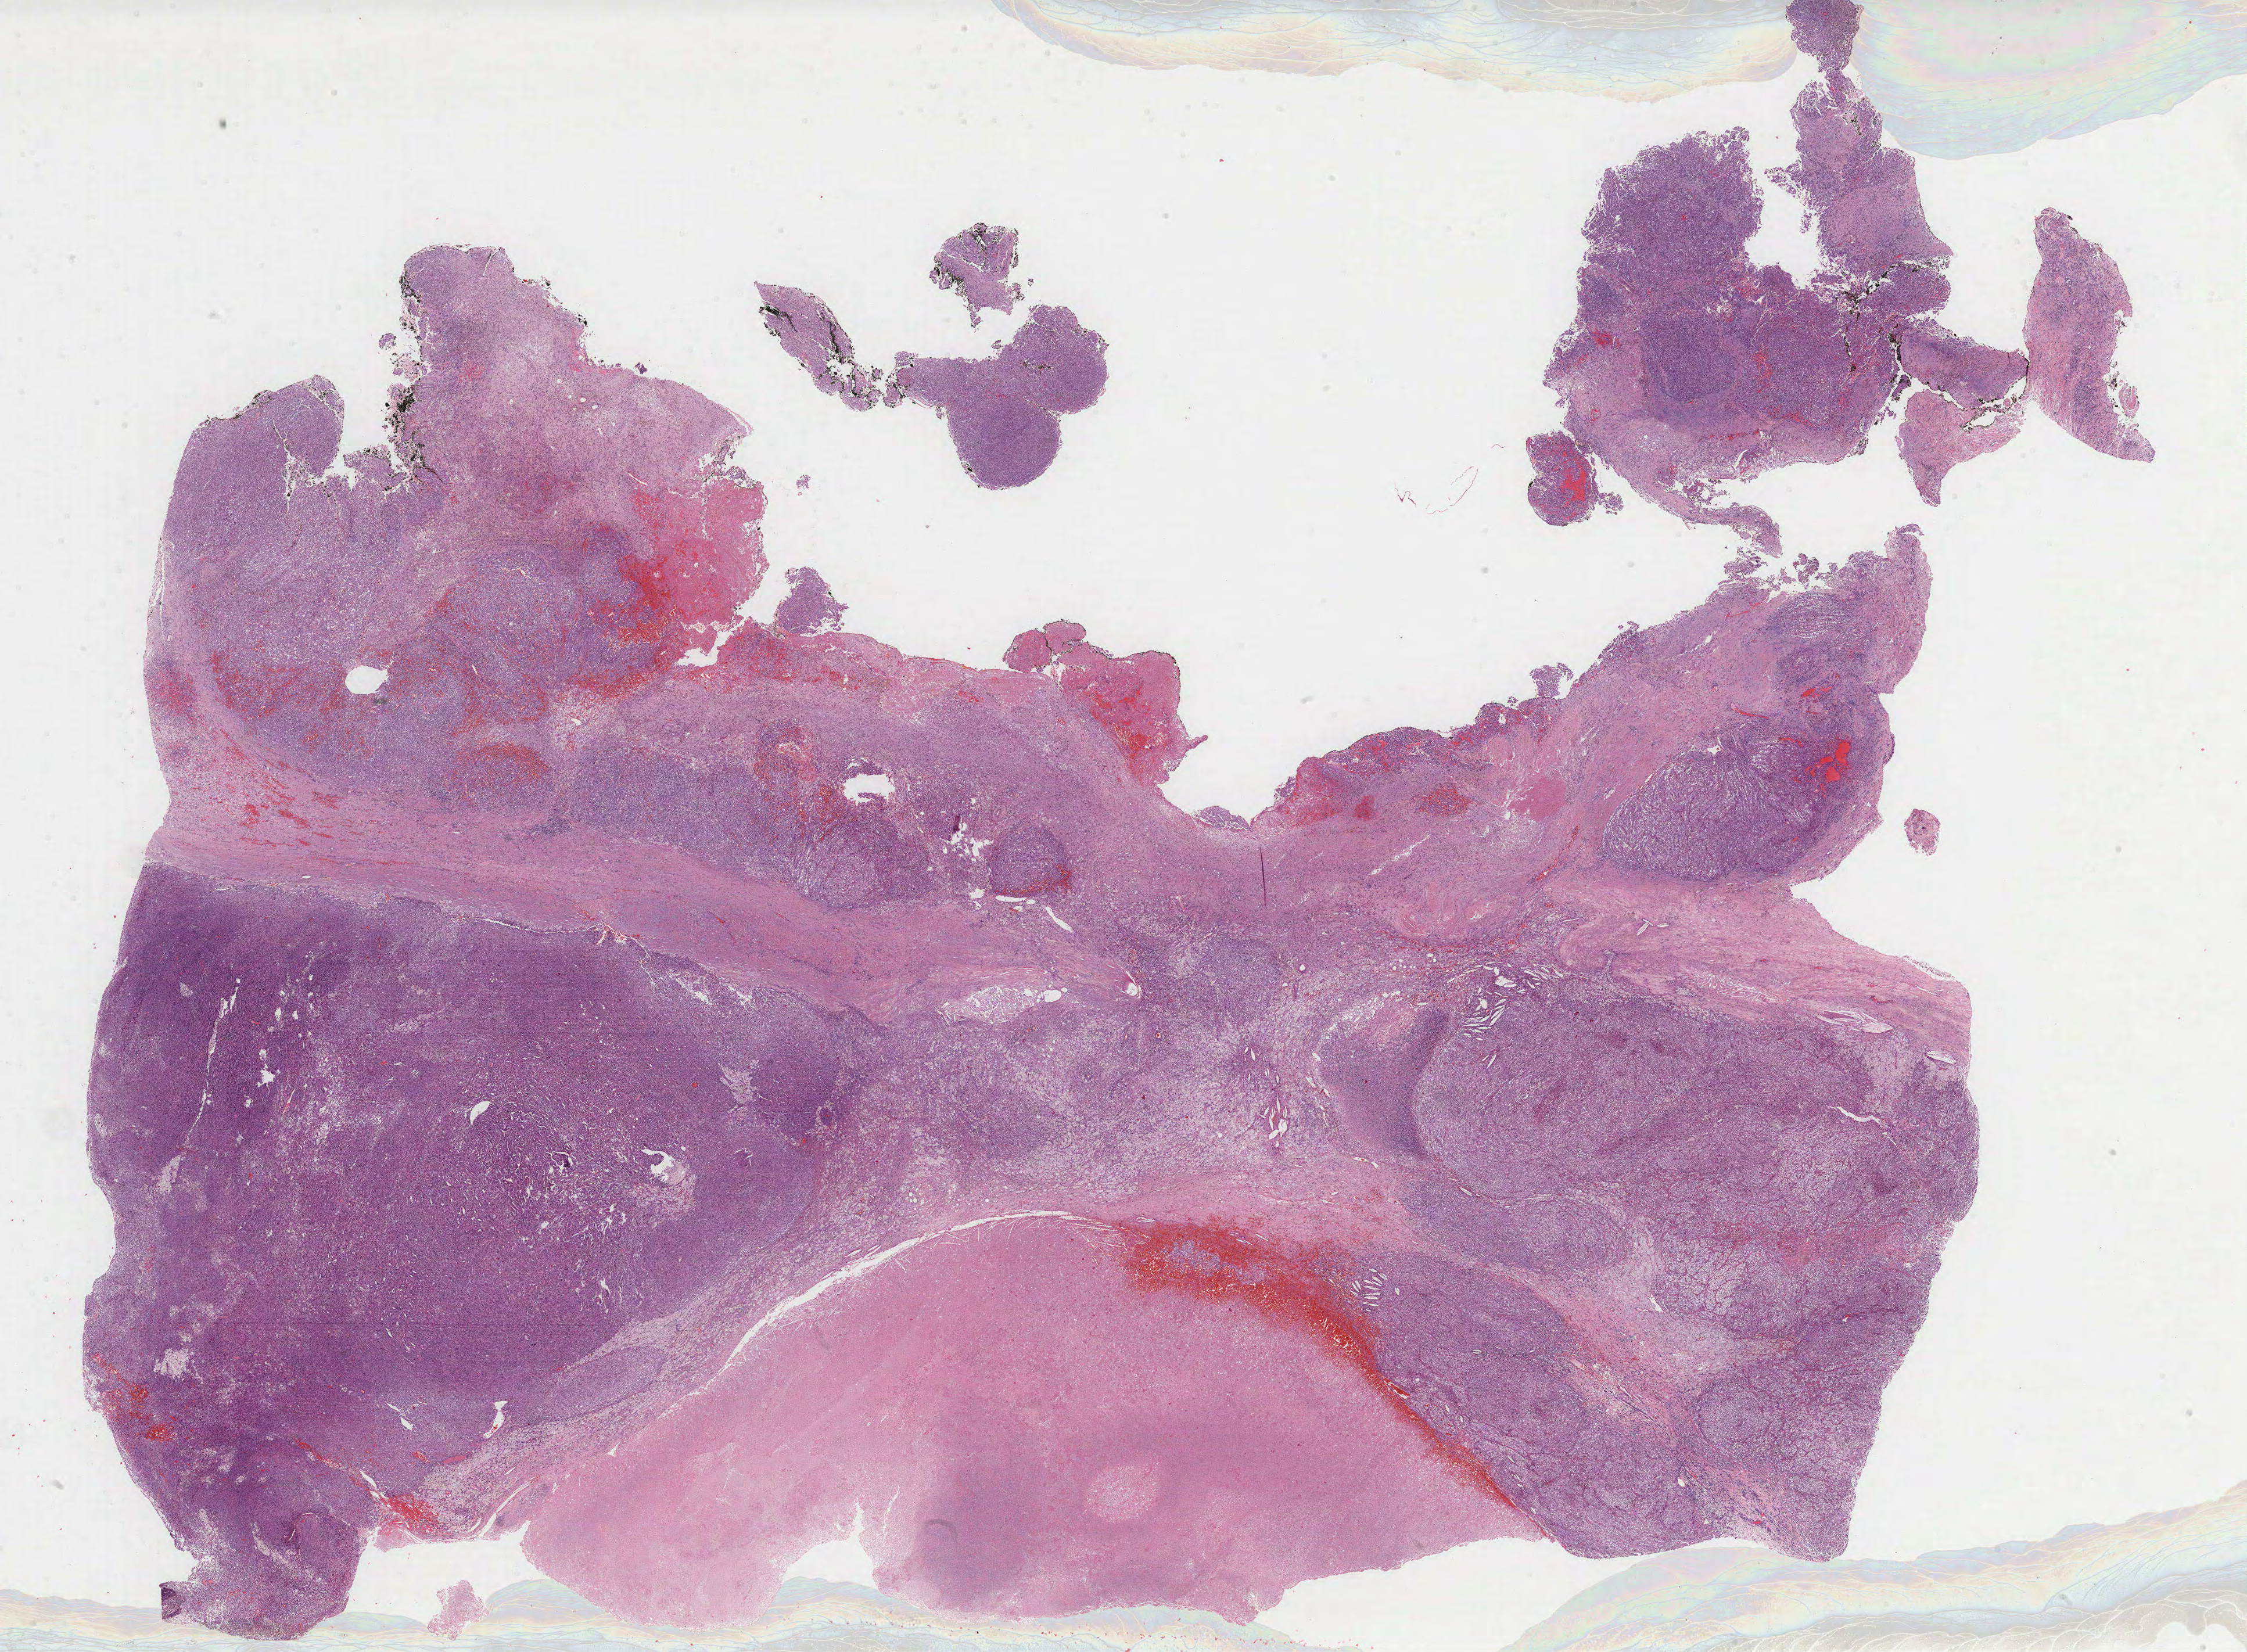
Whole-slide histology image, H&E-stained, low-resolution overview of the scanned area, about 31.2 x 23.0 mm (slide scanned at 40x), formalin-fixed paraffin-embedded (FFPE) diagnostic section, primary tumour sample from the kidney. Male patient; age at initial diagnosis 38 years.
Pathologic diagnosis: Papillary adenocarcinoma, NOS. AJCC pathologic stage: III.